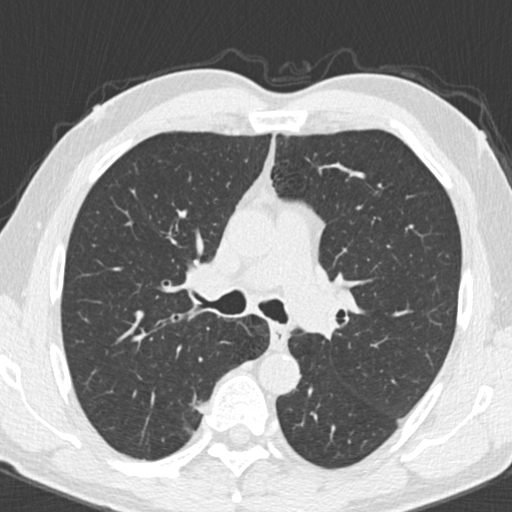
Low-dose screening chest CT, one axial slice; slice 127 of 192 in the series (ordered by position); reconstruction kernel B30f; lung window (W 1500 / L -600 HU); 2 mm slice thickness; 512 × 512 image matrix, field of view 307 × 307 mm.
Outlined on this slice (expert manual segmentation):
- lesion 1 (tumor, upper lobe of right lung): bounding box <193,400,208,413> (left, top, right, bottom; pixels)